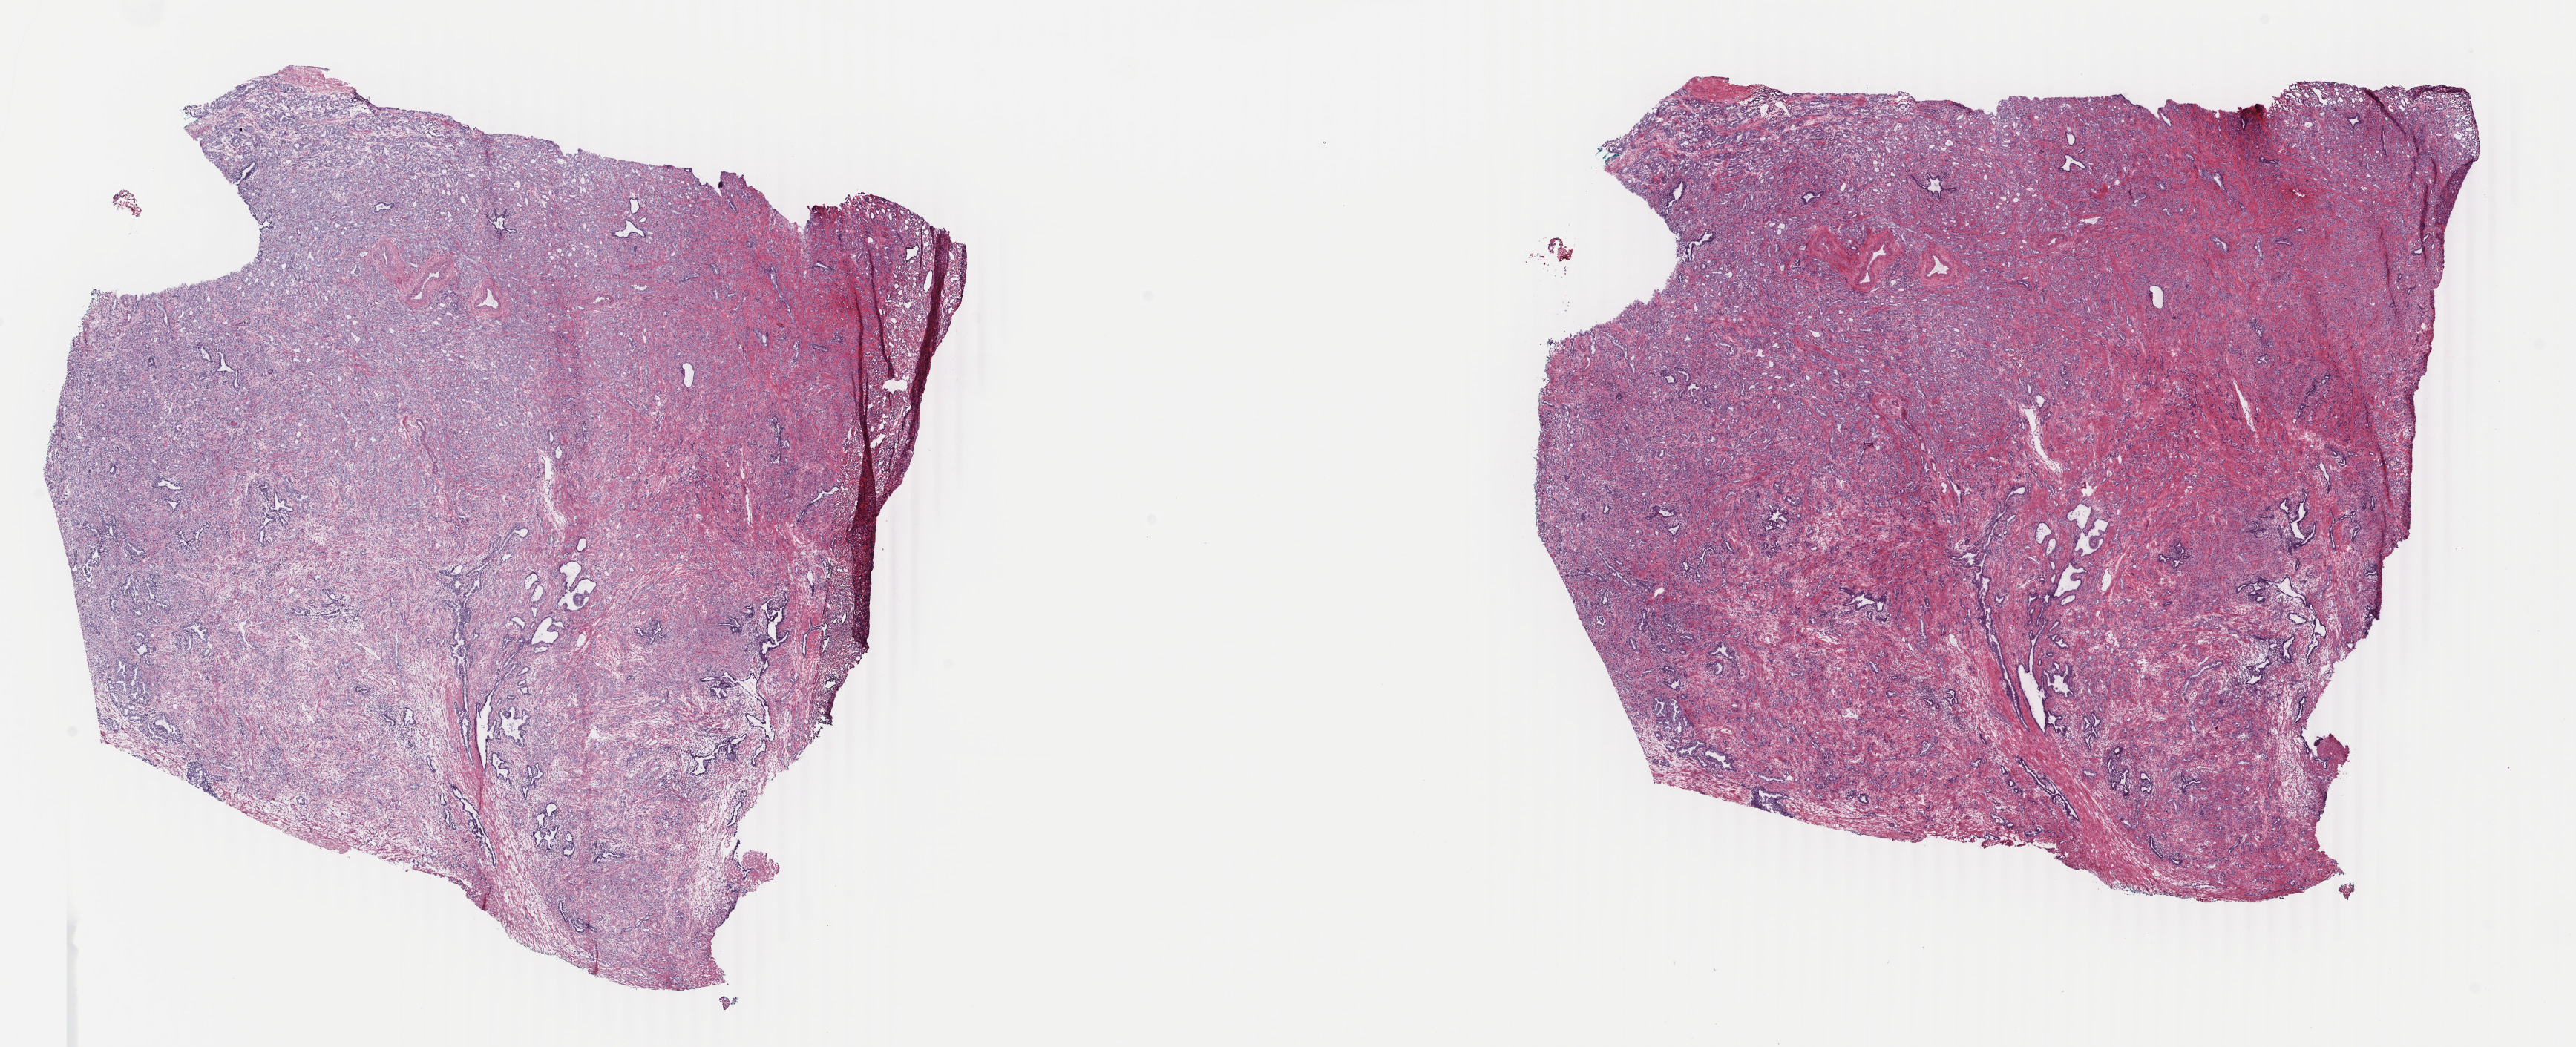
Whole-slide histology image, H&E — whole scanned area (about 27.6 x 11.2 mm, acquisition: 40x scan) shown as a low-resolution overview. Frozen section from the top of the tissue portion. Sample: primary tumour, prostate. Male patient; age at initial diagnosis 55 years. Pathologist review of this section (percent, as recorded): tumour cells 75%, tumour nuclei 85%.
Pathologic diagnosis: Adenocarcinoma, NOS (prostate gland).